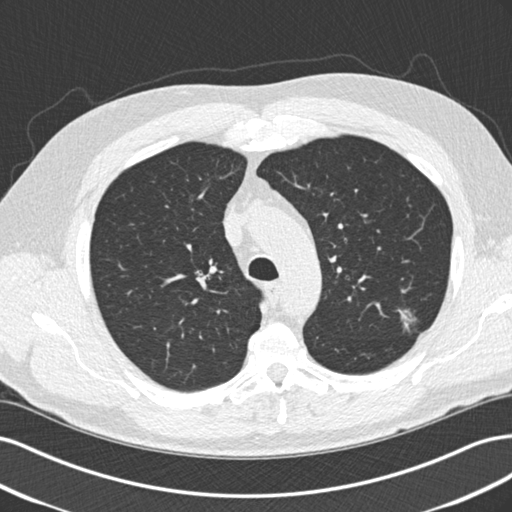
Low-dose screening chest CT, axial slice, second screening round (one year after baseline), lung window (W 1500 / L -600 HU), 2 mm slice thickness, 120 kVp, slice 52 of 209 in the series. Male participant, aged 65 years at enrolment. Former smoker at enrolment.
- Expert-annotated lung lesion, bounding box <388,305,424,338> (left, top, right, bottom; pixels).
- The exam's reader record, not a measurement of the box and not confirmed to be the same lesion: non-calcified nodule or mass ≥4 mm, left upper lobe, 10 × 9 mm, poorly defined margins, mixed attenuation, pre-existing on the prior screen: yes; interval growth: no.
- Official screen result: positive, other.